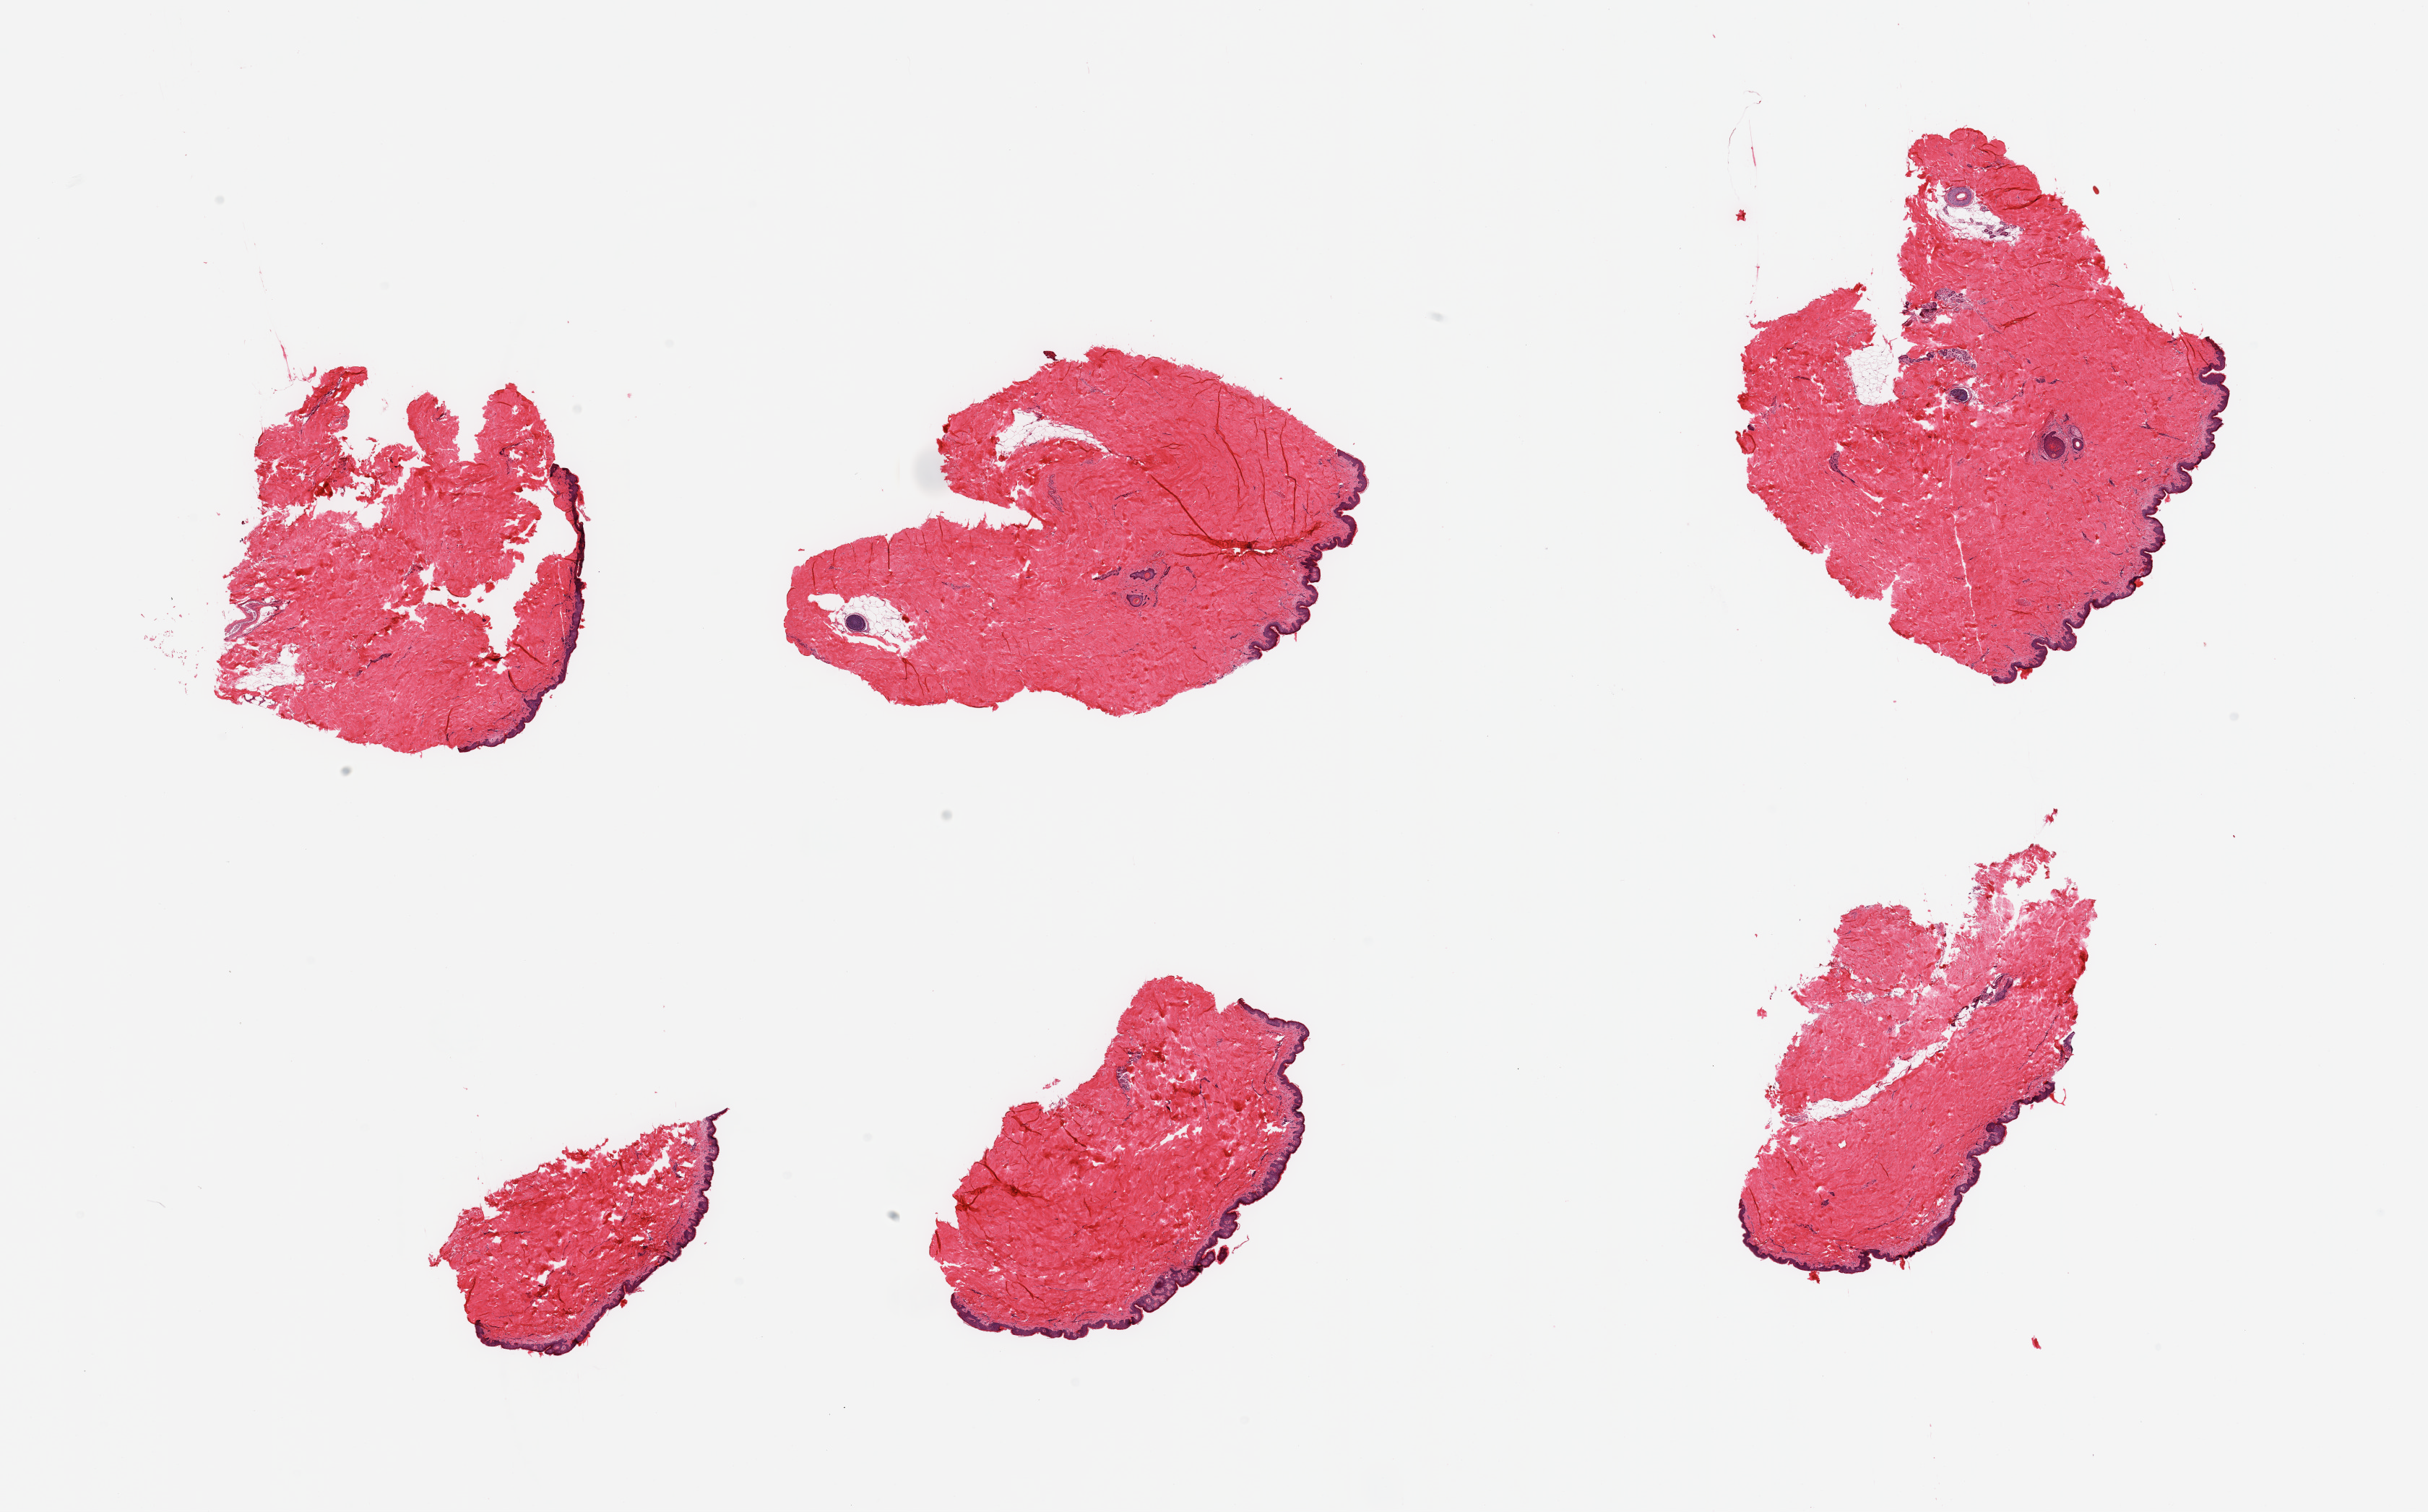
Whole-slide image, hematoxylin and eosin (H&E) stain, low-resolution overview of the scanned area, about 26.6 x 16.6 mm (slide scanned at 20x). PAXgene-fixed, paraffin-embedded tissue. Sampled site (target tissue): skin of suprapubic region. Donor tissue sample. Donor: male.
Pathologist's review note for this sample: 6 pieces; ~10% to 15% internal fat on 4 of 6 pieces, few tissue defects.